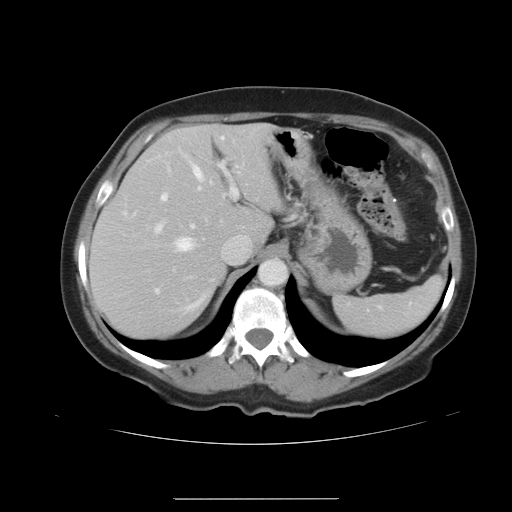
Contrast-enhanced abdominal CT, one axial slice; slice 27 of 41 in the series (ordered by position); 120 kVp; intravenous contrast given; soft-tissue window (W 400 / L 40 HU); 5 mm slice thickness; 512 × 512 image matrix, field of view 381 × 381 mm. Female patient, age 63 years. Case-level facts recorded for this patient, not image findings: diagnosis: colorectal cancer liver metastases, imaged before liver resection; multiple liver metastases: yes; largest metastasis: 1.5 cm.
Annotated regions visible in this slice (outlined manually by an expert reader):
- hepatic veins: bounding box <175,137,224,251> (left, top, right, bottom; pixels)
- liver: <90,124,280,341>
- planned liver remnant (the part of the liver to remain after resection): <90,124,280,341>
- portal vein (with intrahepatic branches): <155,161,237,292>